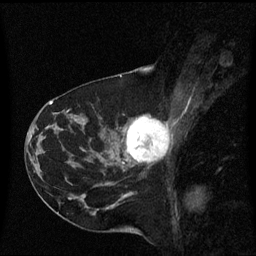
Breast MRI (dynamic contrast-enhanced), one sagittal slice. Position 30 of 60 along the scan axis. Dynamic contrast-enhanced series, image 2 of 3 at this slice position (ordered by acquisition). 1.5 T. TE 4.2 ms, TR 8.4 ms. 256 × 256 image matrix, field of view 220 × 220 mm. Female patient, age 41 years. Case-level facts recorded for this patient, not image findings: setting: breast cancer imaged before/during neoadjuvant chemotherapy; receptor status: triple-negative.
Structures marked on this image (semi-automatic segmentation, software-assisted and operator-edited):
- analysis volume of interest (the breast-tissue region the enhancement analysis was run in; not a lesion): bounding box <116,116,172,171> (left, top, right, bottom; pixels)
- tumour enhancement mask (voxels above the 70 % enhancement threshold inside the analysis volume of interest): <126,116,169,163>